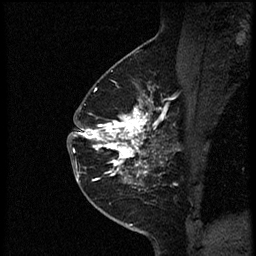
Breast MRI (dynamic contrast-enhanced), one sagittal slice; slice 37 of 56 in the series (ordered by position); dynamic contrast-enhanced study with each time point stored as its own series, time point 2 of 4 at this slice position (early post-contrast, ordered by acquisition time); 1.5 T; TE 4.2 ms, TR 18.9 ms; 2 mm slice thickness; 256 × 256 image matrix, field of view 200 × 200 mm. Female patient. From the clinical record (not read from this slice): setting: breast cancer imaged before/during neoadjuvant chemotherapy; receptor status: HER2-positive.
Structures marked on this image (semi-automatically segmented with operator editing):
- analysis volume of interest (the breast-tissue region the enhancement analysis was run in; not a lesion): bounding box <78,85,174,189> (left, top, right, bottom; pixels)
- tumour enhancement mask (voxels above the 100 % enhancement threshold inside the analysis volume of interest): <78,85,165,184>